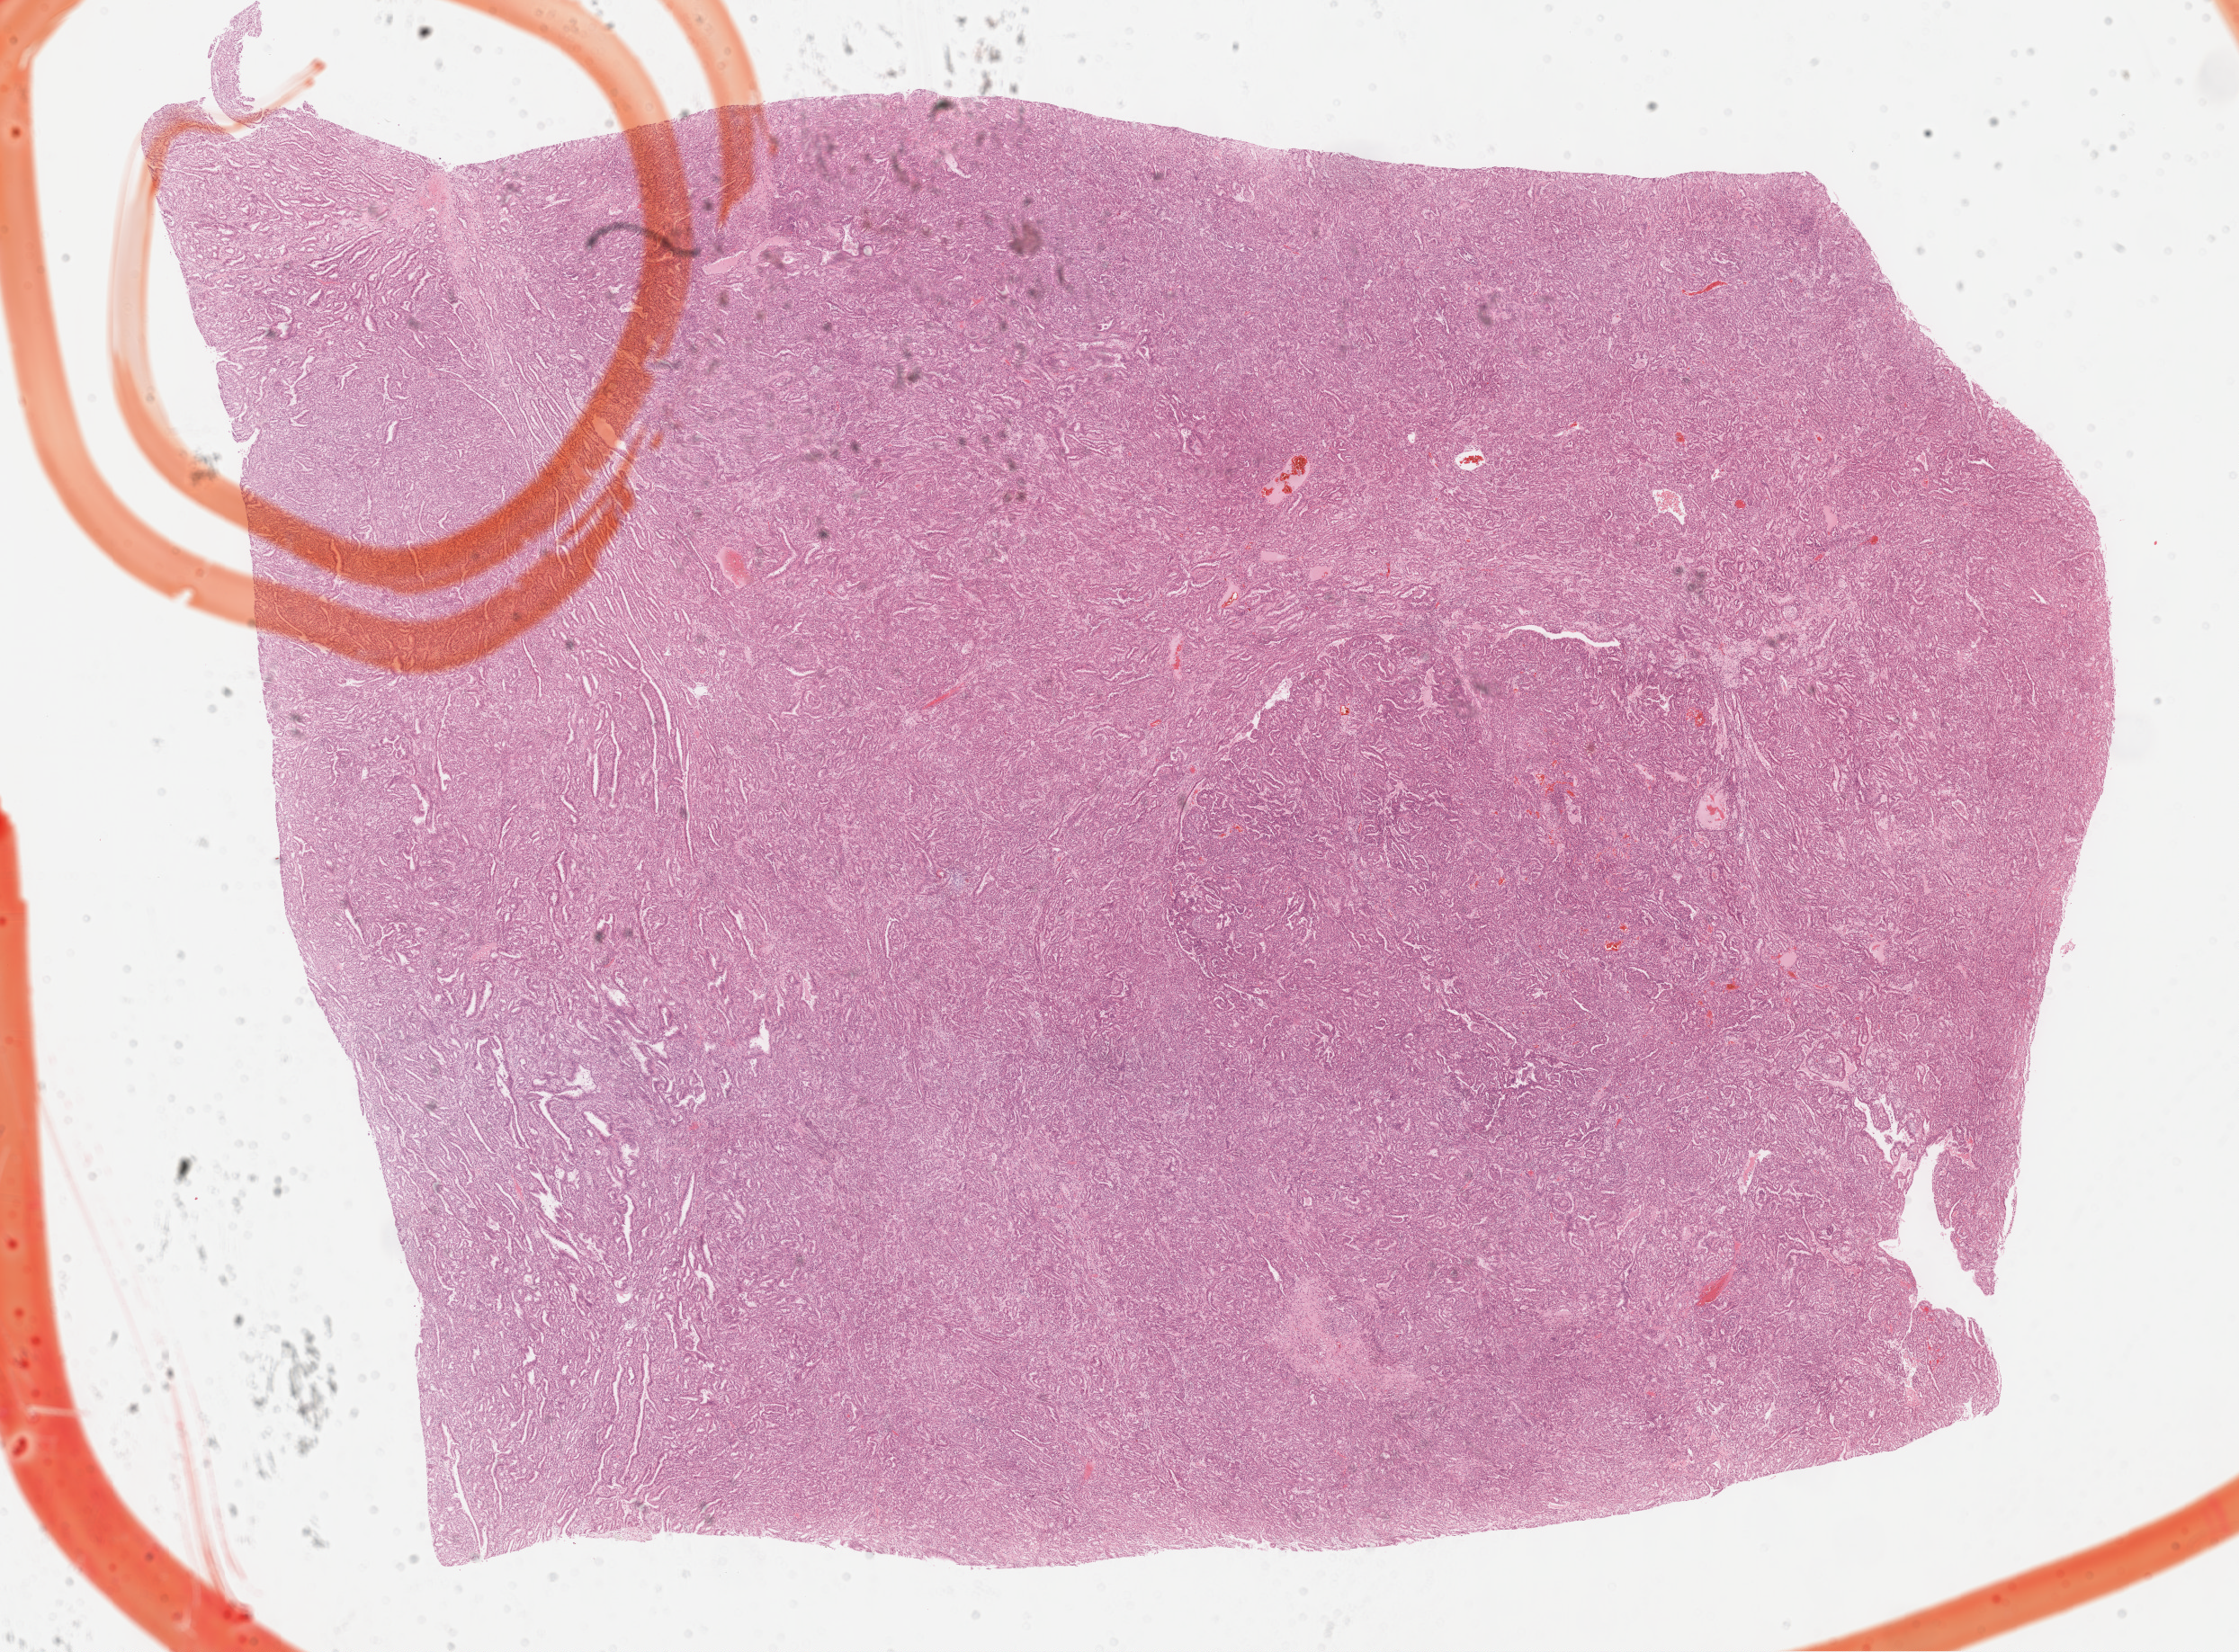
H&E whole-slide image — shown as a low-resolution overview of the whole scanned area (about 20.1 x 14.9 mm, slide scanned at 40x), formalin-fixed paraffin-embedded (FFPE) diagnostic section, sample: primary tumour, kidney. Patient: female, age at initial diagnosis 37 years.
AJCC pathologic stage: I. Laterality: left. Histologic diagnosis: Papillary adenocarcinoma, NOS.